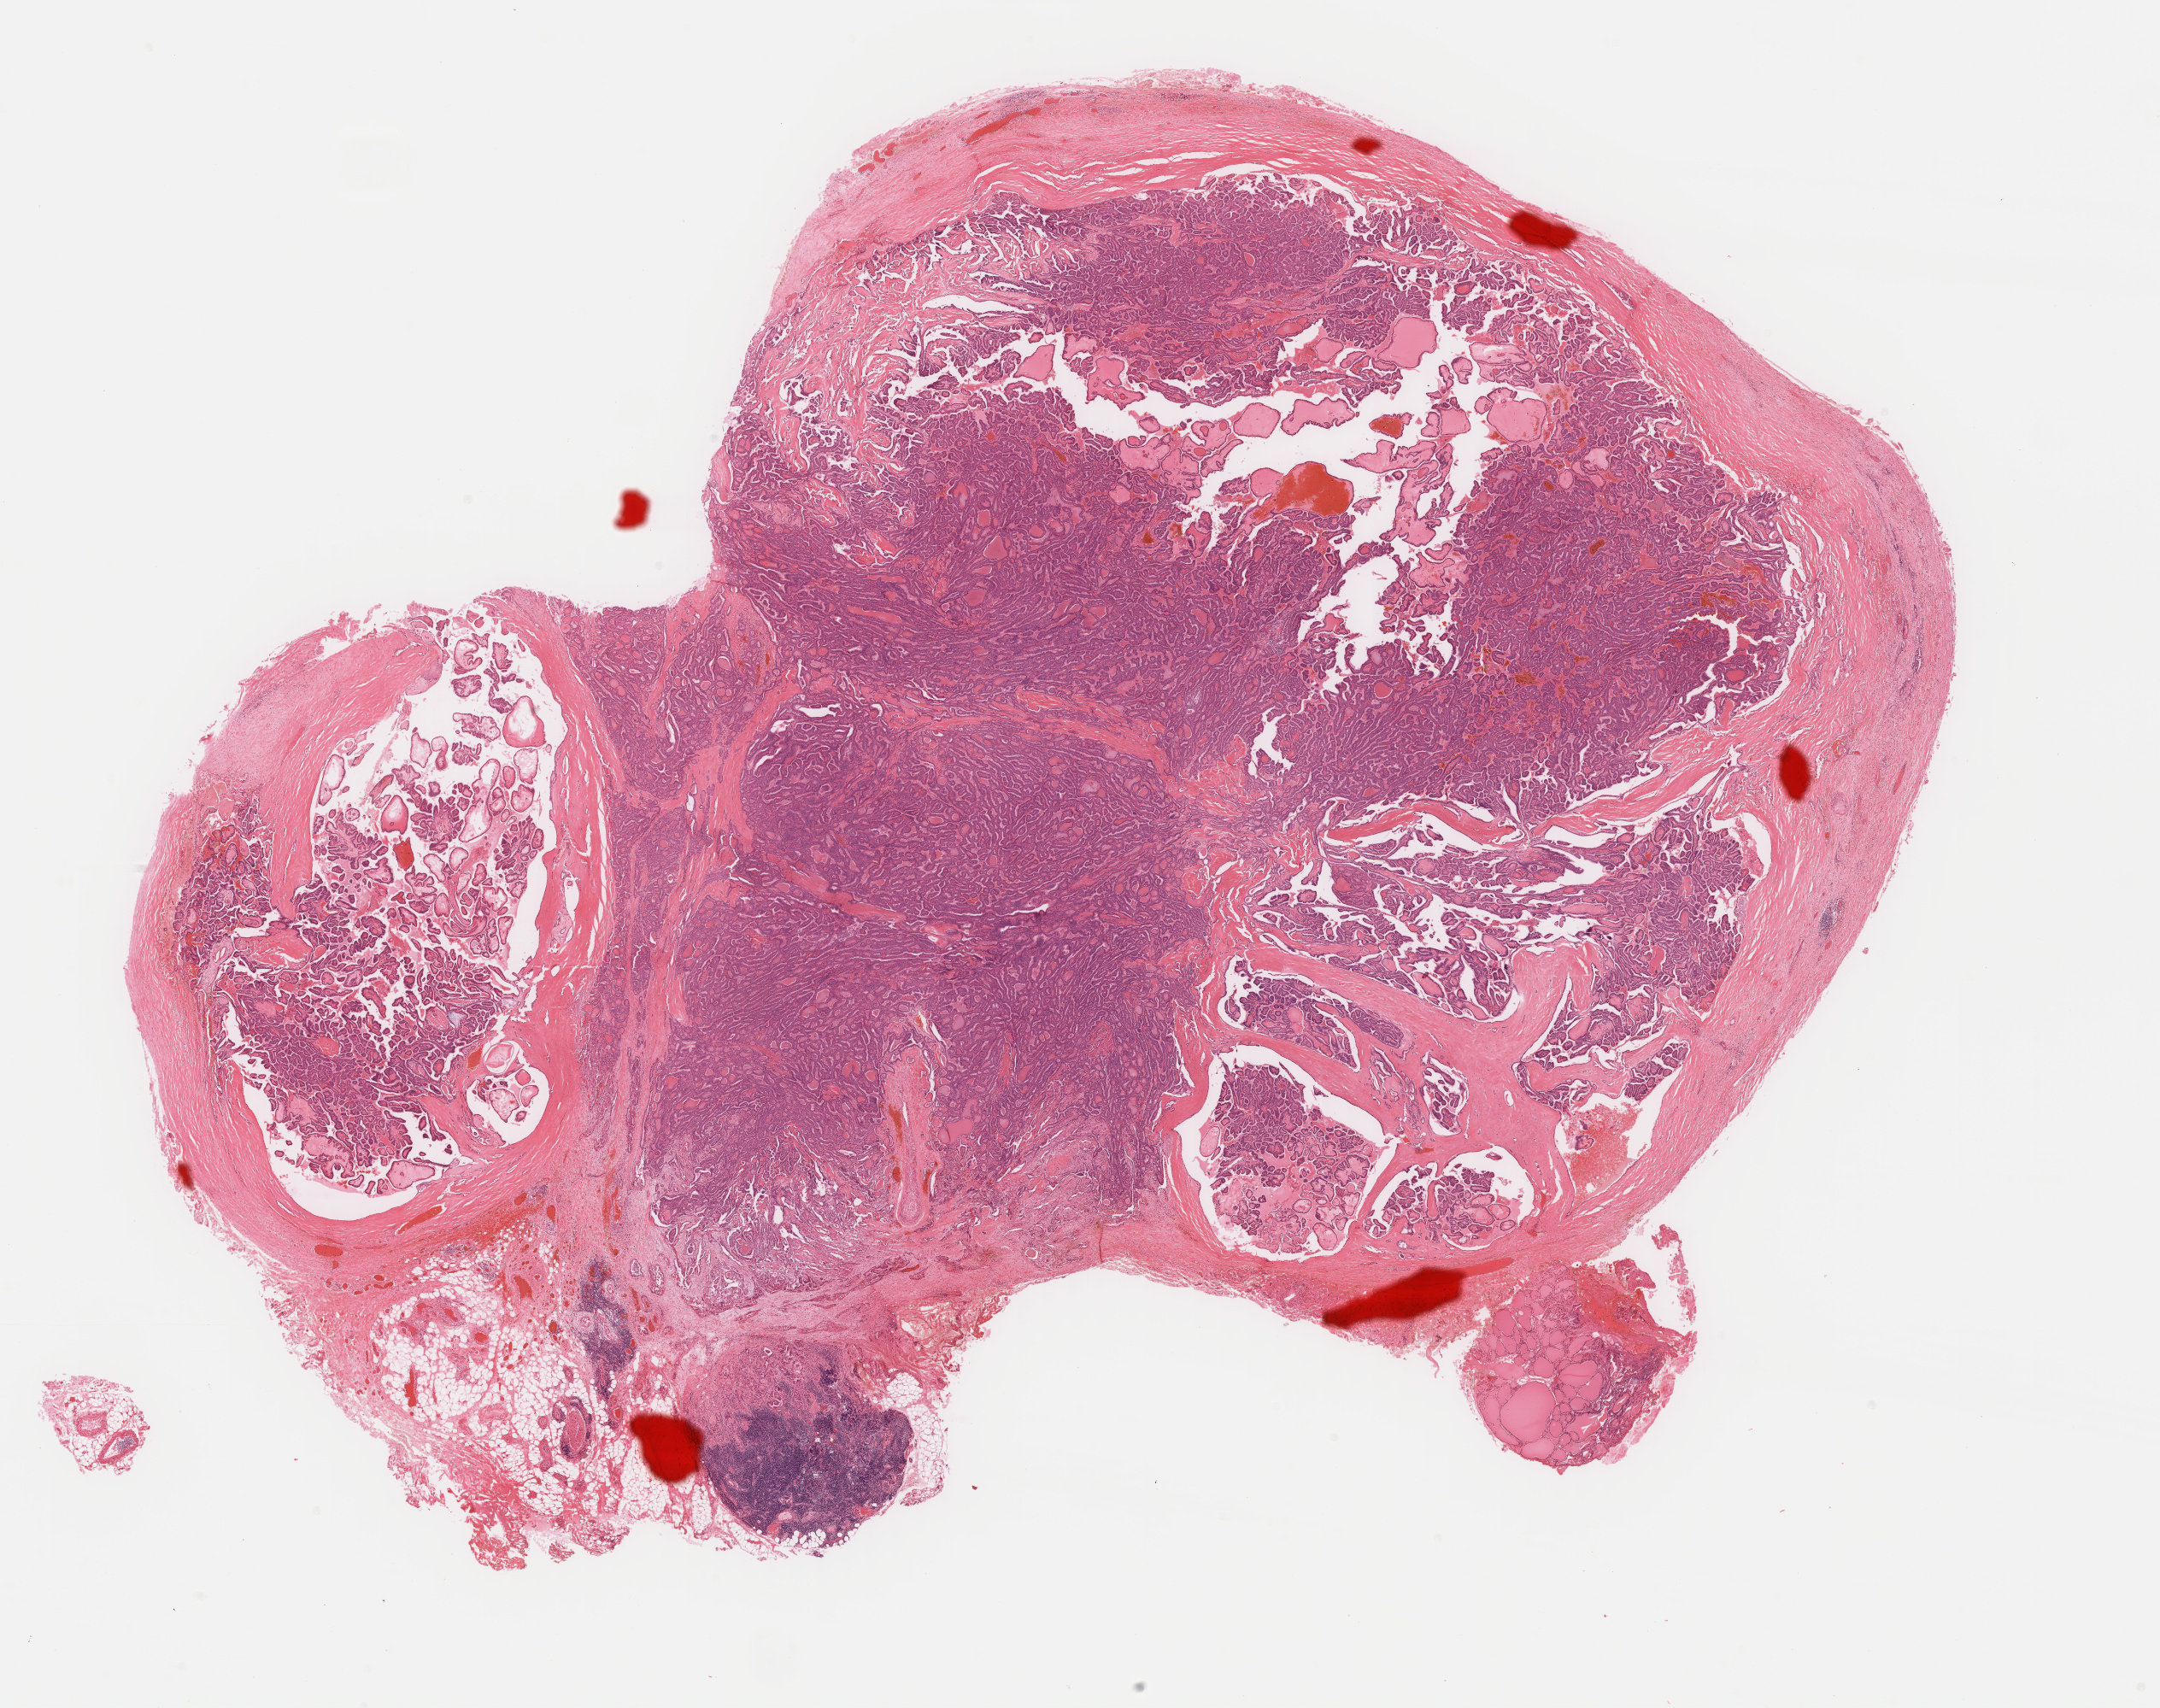
Whole-slide histology image, Hematoxylin and eosin (H&E) stained — a low-resolution overview of the entire scanned area, about 20.1 x 15.9 mm (from a 40x scan); formalin-fixed paraffin-embedded (FFPE) diagnostic section; primary tumour sample from the thyroid. Patient: female, age at initial diagnosis 25 years.
- TNM: T2 N0 M0
- AJCC pathologic stage: I (7th edition)
- laterality: right
- lymph nodes positive (case pathology): 0 of 2 examined
- pathologic diagnosis: Papillary adenocarcinoma, NOS (thyroid gland)